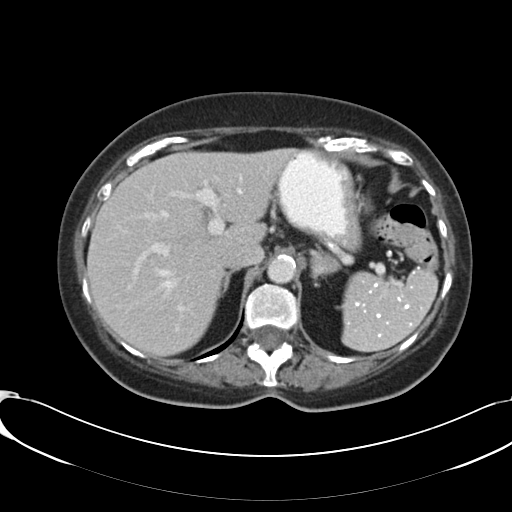
Contrast-enhanced abdominal CT, one axial slice. Position 74 of 91 along the scan axis. 120 kVp. Intravenous contrast given. Soft-tissue window (W 400 / L 40 HU). 512 × 512 image matrix. Patient: female, 73 years. Case-level facts recorded for this patient, not image findings: diagnosis: adrenocortical carcinoma; tumour side: left adrenal; tumour size at pathology: 4.9 cm.
Annotated regions visible in this slice (semi-automatically segmented with operator editing):
- mass: box from (x=311, y=254) to (x=340, y=279) px